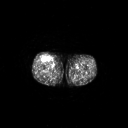
FDG PET of an extremity soft-tissue mass (from a PET/CT study), one axial slice. Slice 262 of 311 in the series (ordered by position). 3.27 mm slice thickness. 128 × 128 image matrix, field of view 700 × 700 mm. Male patient, age 56 years. Case-level facts recorded for this patient, not image findings: histological type: pleiomorphic leiomyosarcoma; grade: intermediate; site of the primary tumour: right thigh.
Outlined on this slice (expert contour drawn on MRI and transferred to this co-registered scan by the dataset authors):
- gross tumour volume including surrounding oedema: box from (x=41, y=55) to (x=51, y=62) px